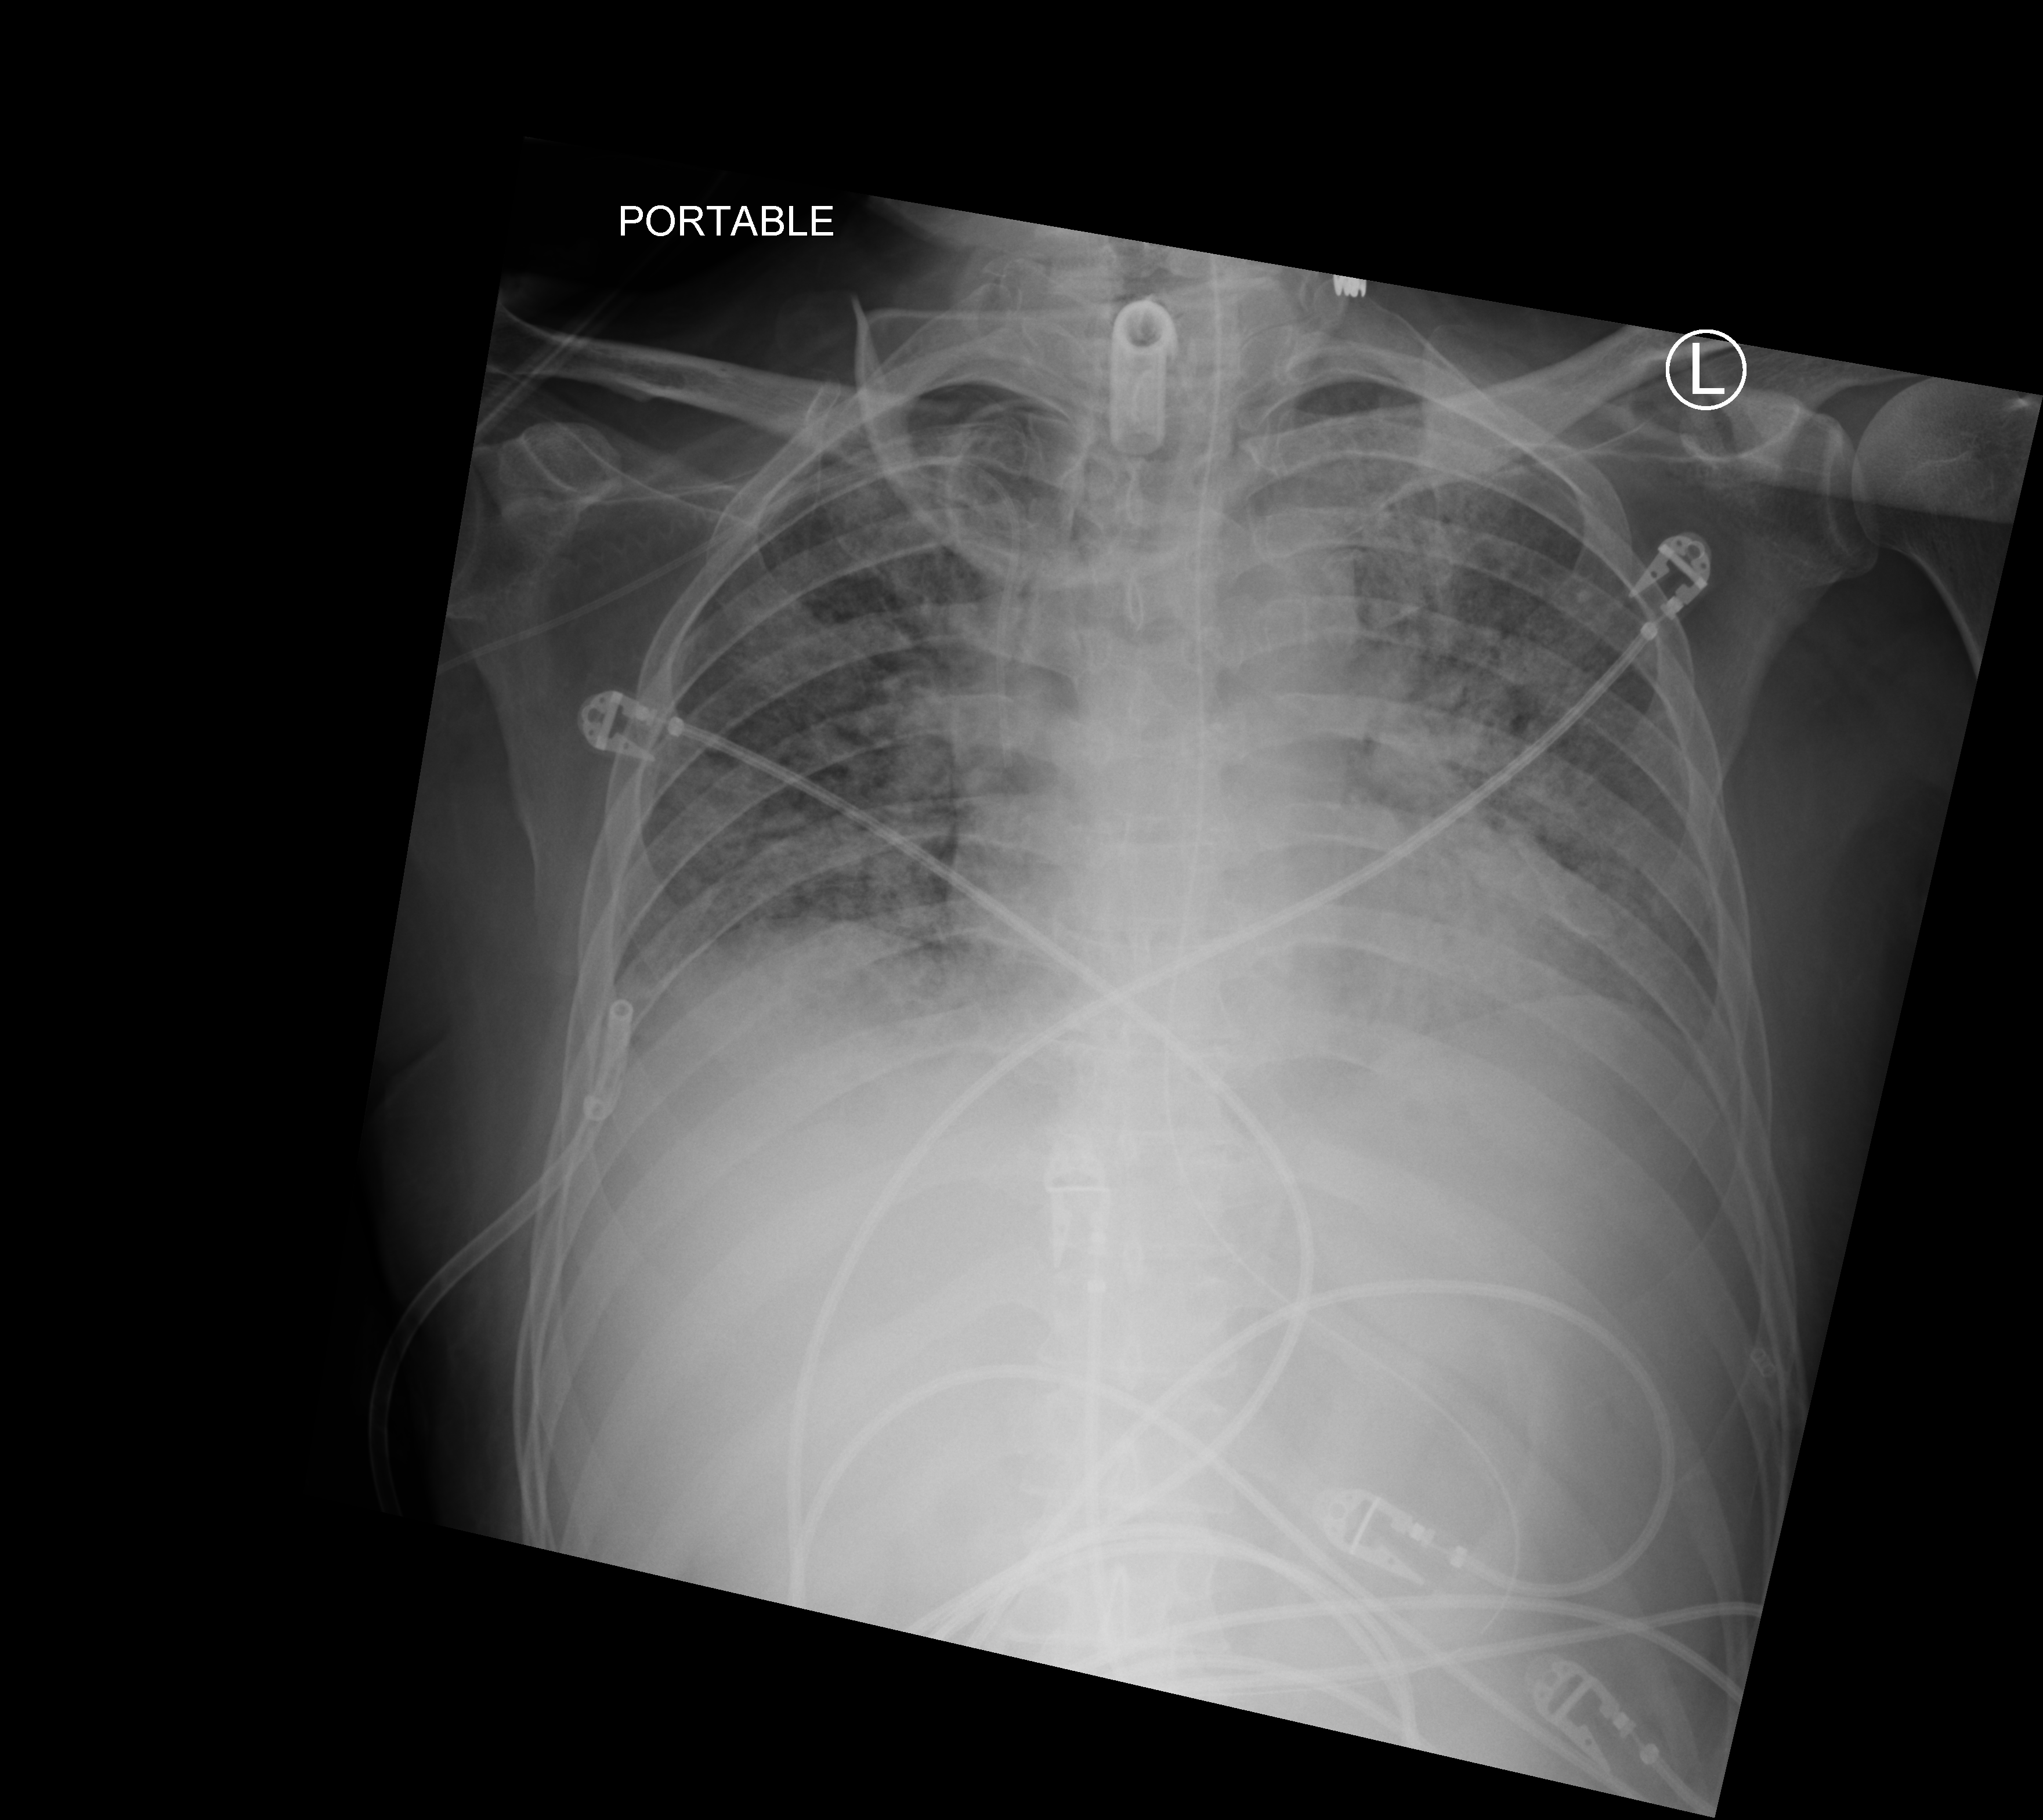
Bedside chest radiograph (computed radiography); anteroposterior (AP) projection. Patient hospitalised with COVID-19; male, aged 18–59 years.
From the hospital-stay record, not from the radiograph (when in the stay this image was taken is not recorded): admitted to intensive care during this hospital stay: yes; mechanically ventilated during this hospital stay: yes; length of hospital stay: 77 days.